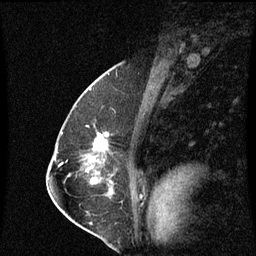
Breast MRI (dynamic contrast-enhanced), one sagittal slice; position 39 of 60 along the scan axis; dynamic contrast-enhanced series, image 2 of 3 at this slice position (ordered by acquisition); 1.5 T; TE 4.2 ms, TR 8.9 ms; 256 × 256 image matrix, field of view 200 × 200 mm. Patient: female, 57 years. From the clinical record (not read from this slice): setting: breast cancer imaged before/during neoadjuvant chemotherapy; receptor status: HR-positive, HER2-negative.
Annotated regions visible in this slice (semi-automatically segmented with operator editing):
- analysis volume of interest (the breast-tissue region the enhancement analysis was run in; not a lesion): bounding box [x1, y1, x2, y2] px = [83, 124, 110, 159]
- tumour enhancement mask (voxels above the 70 % enhancement threshold inside the analysis volume of interest): [96, 136, 106, 149]